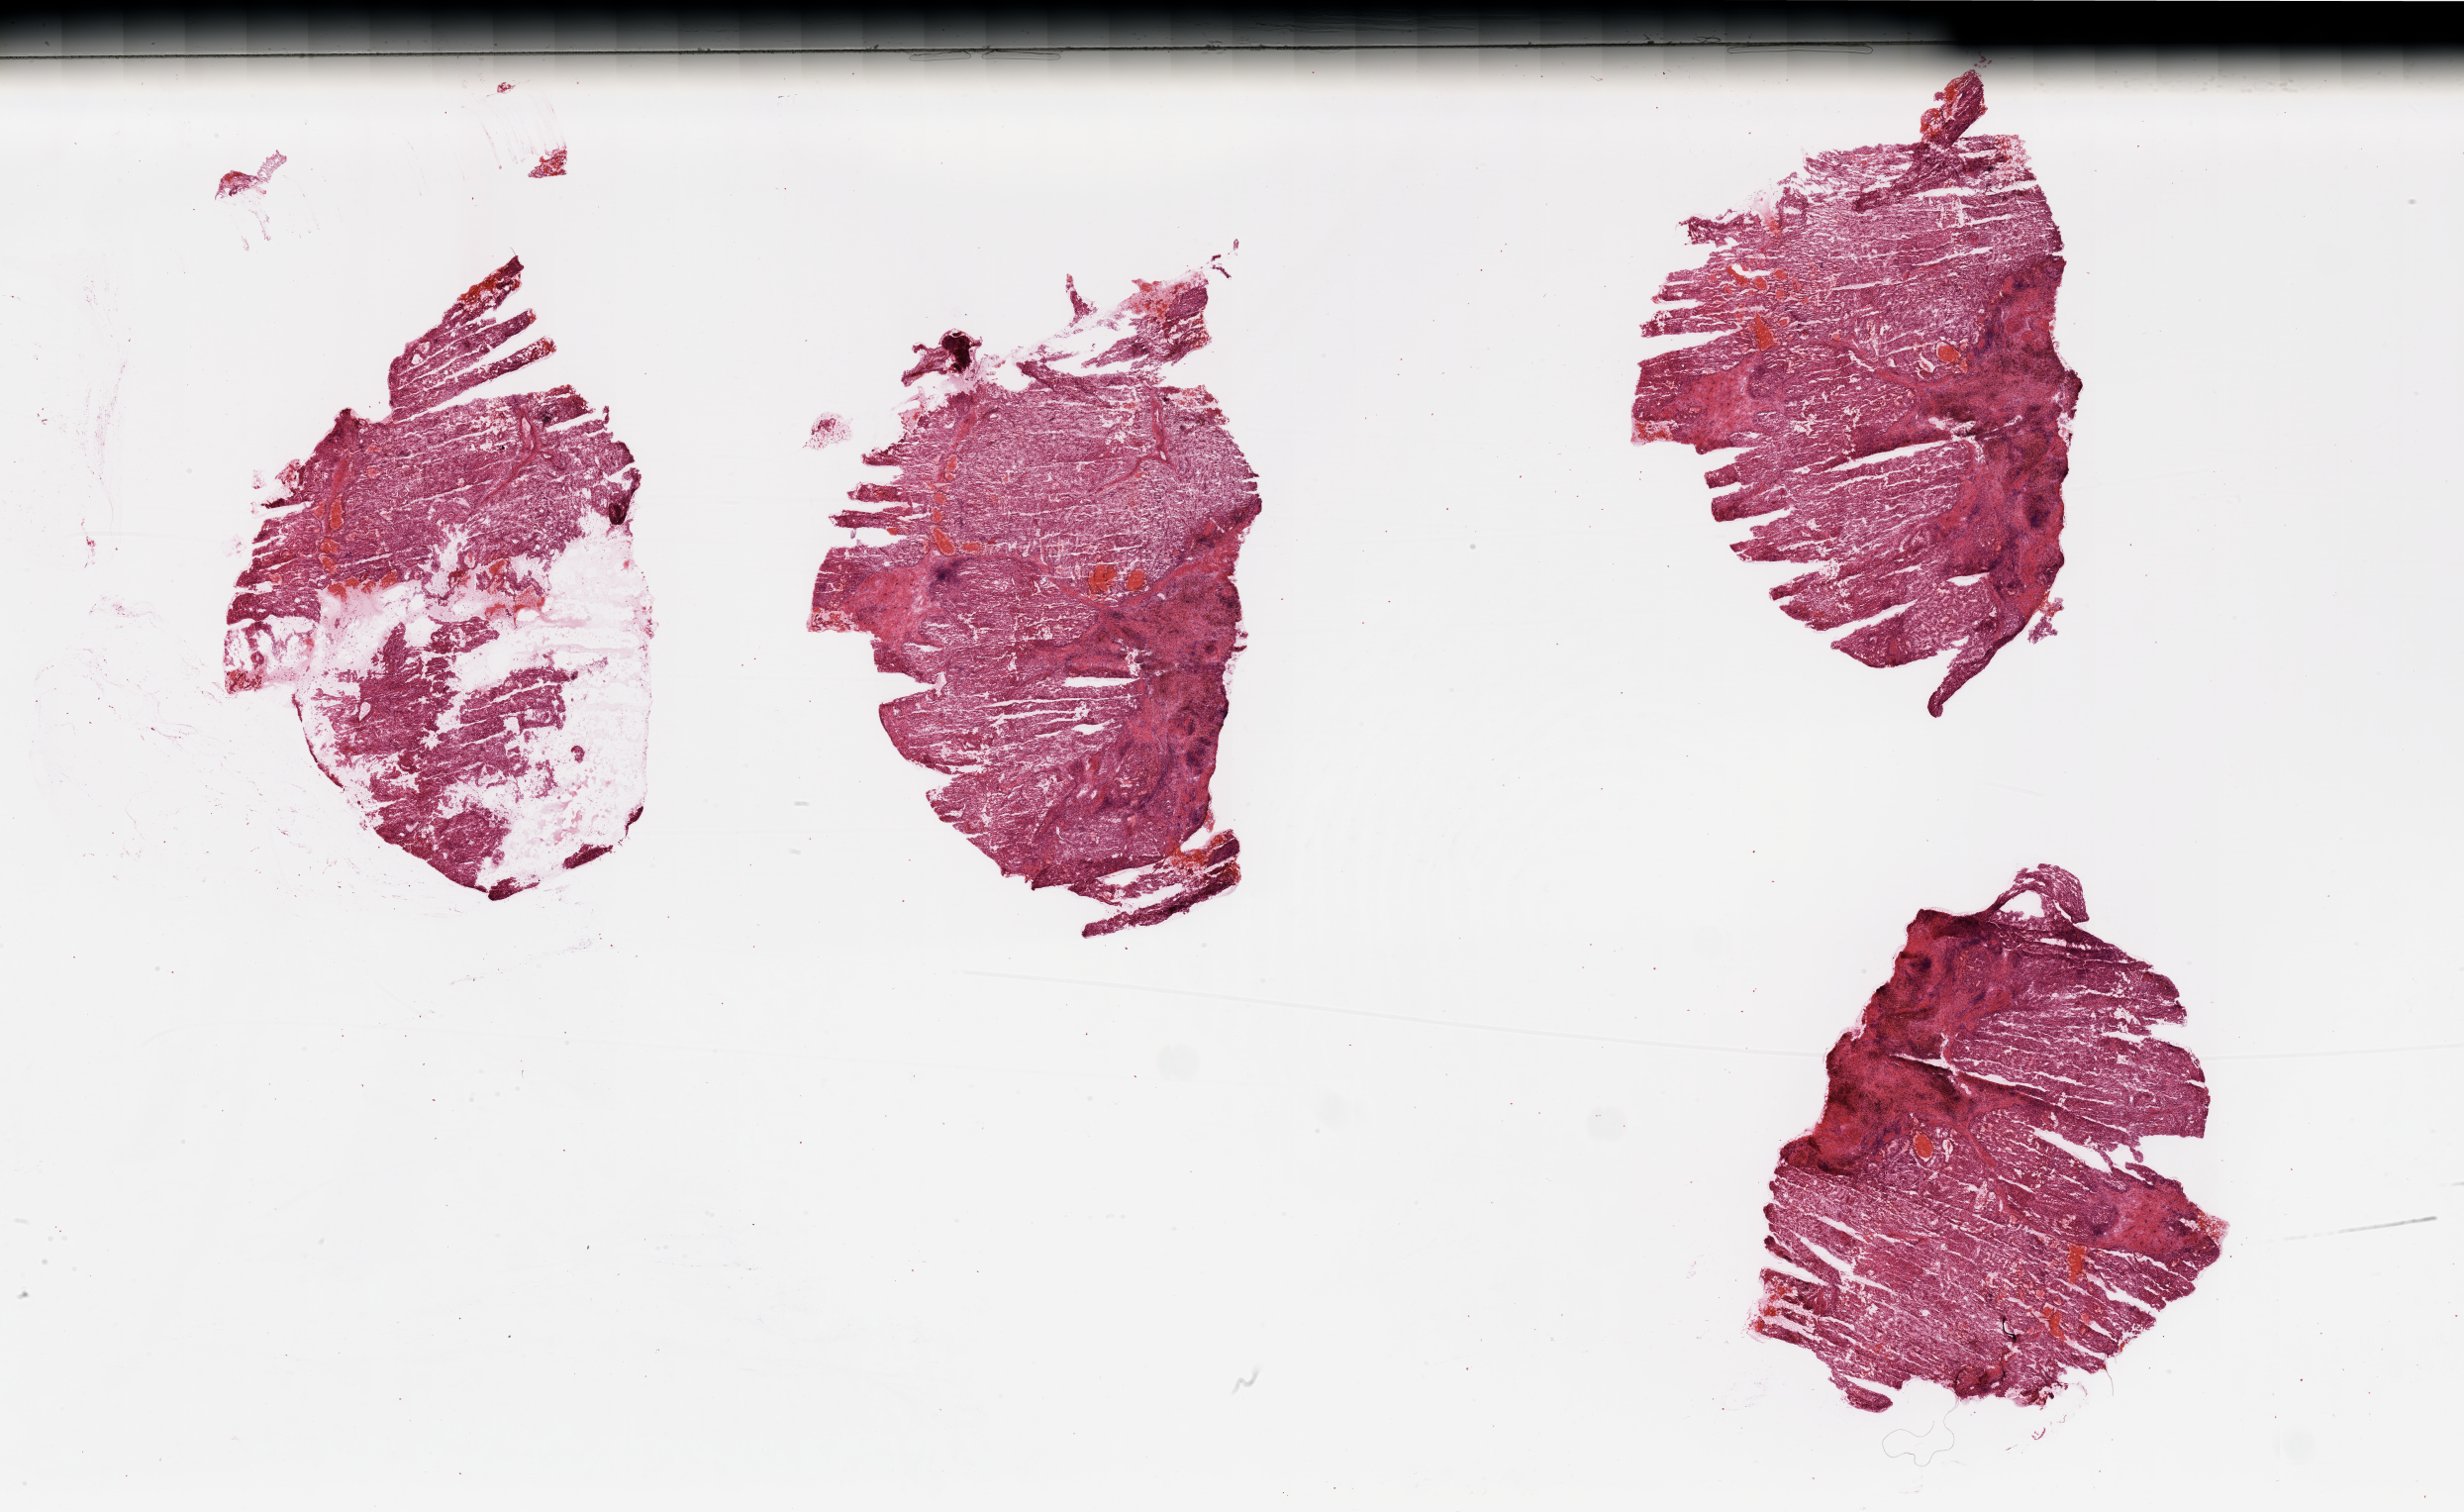
Whole-slide histology image, H&E-stained — shown as a low-resolution overview of the whole scanned area (about 39.4 x 24.2 mm, acquisition: 20x scan); tumour tissue sample, sampled site: kidney. 54-year-old male patient. Histologic grade: G2 (moderately differentiated). Composition of this section per pathologist review: tumour nuclei 80%, necrosis 5%.
- diagnosis: Renal cell carcinoma, NOS
- AJCC pathologic stage: IV
- primary tumour site (as recorded): upper pole